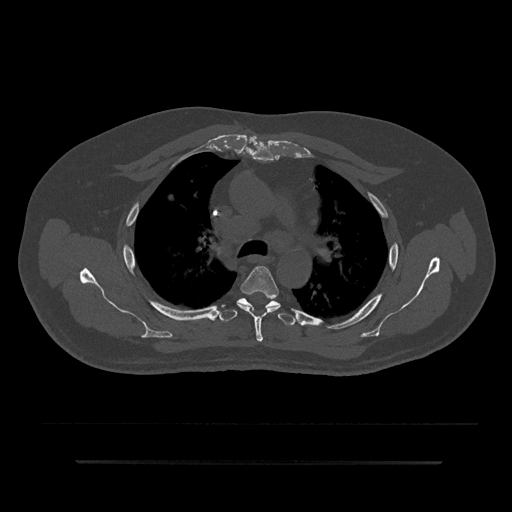
CT including the spine, one axial slice. Slice 602 of 797 in the series (ordered by position). Reconstruction kernel Br40s/3. Bone window (W 1800 / L 400 HU). 512 × 512 image matrix, field of view 464 × 464 mm. Male patient, age 59 years. Case-level facts recorded for this patient, not image findings: primary cancer: bile ducts; vertebrae with lytic lesions (as recorded): T10.
Annotated regions visible in this slice (semi-automatic segmentation, software-assisted and operator-edited):
- T4 vertebra: bounding box (x1, y1, x2, y2) in pixels: (237, 266, 280, 342)
- T5 vertebra: (219, 298, 297, 326)